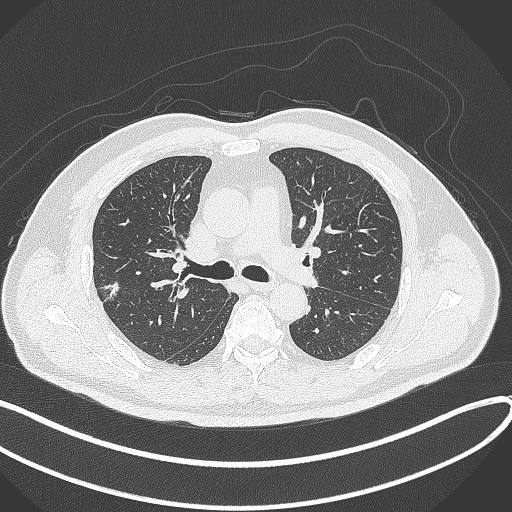
Chest CT, one axial slice; slice 213 of 372 in the series (ordered by position); reconstruction kernel B70f; 120 kVp; lung window (W 1500 / L -600 HU); 1 mm slice thickness; 512 × 512 image matrix, field of view 400 × 400 mm. Male patient, age 60 years. Case-level facts recorded for this patient, not image findings: clinical TNM (as recorded): T1c N0 M0.
Structures marked on this image (bounding box drawn by a radiologist):
- lung tumour (recorded histology: adenocarcinoma): bounding box (x1, y1, x2, y2) in pixels: (94, 275, 123, 305)